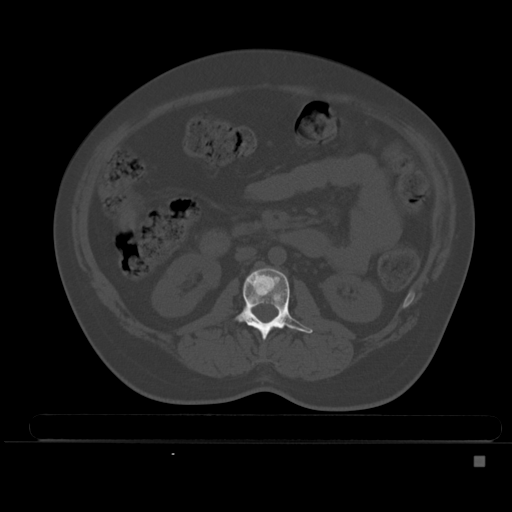
CT including the spine, one axial slice. Position 173 of 495 along the scan axis. Bone window (W 1800 / L 400 HU). 1.5 mm slice thickness. 512 × 512 image matrix. Female patient, age 33 years. Case-level facts recorded for this patient, not image findings: primary cancer: breast; vertebrae with lytic lesions (as recorded): T1.
Structures marked on this image (semi-automatic segmentation, software-assisted and operator-edited):
- L2 vertebra: bounding box <234,268,313,339> (left, top, right, bottom; pixels)